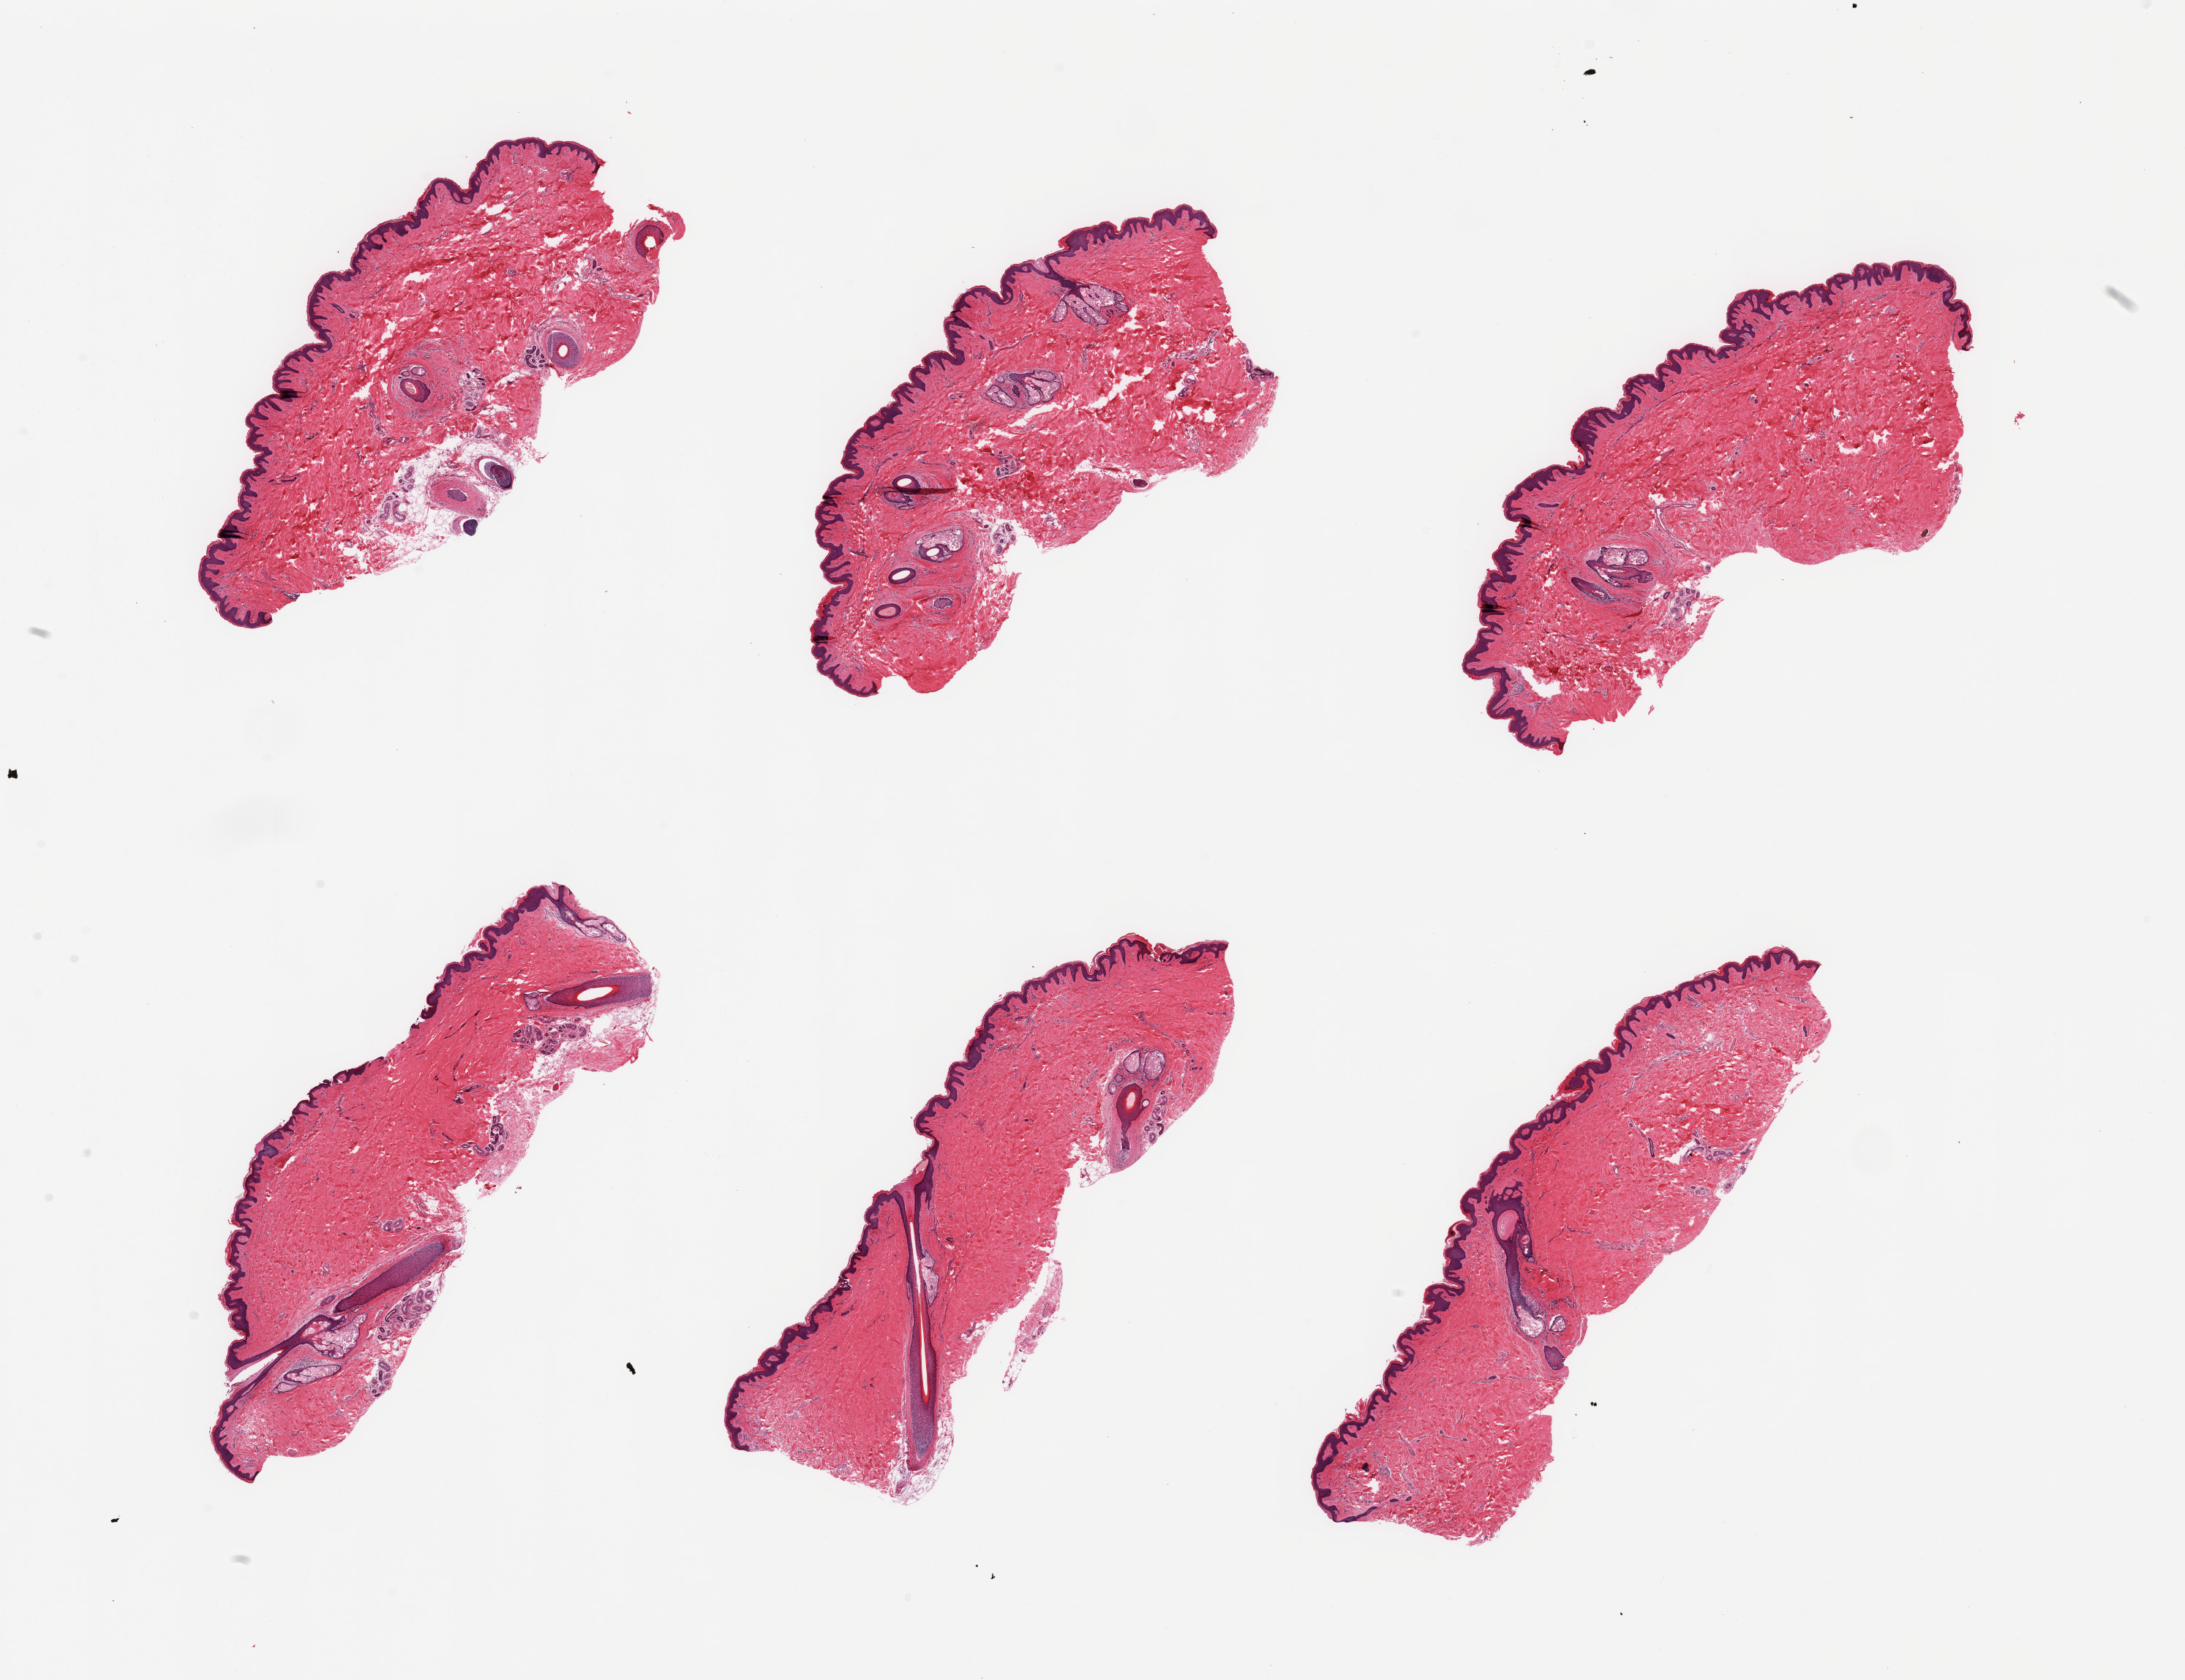
Digitized haematoxylin and eosin-stained section, brightfield — shown as a low-resolution overview of the whole scanned area (about 23.6 x 18.2 mm), PAXgene-fixed paraffin-embedded (PFPE) section, target tissue: skin of suprapubic region, donor tissue sample. Donor sex: male.
Reviewer comment on this tissue sample: 6 pieces; no dermal fat; squamous epithelium is ~40 microns.